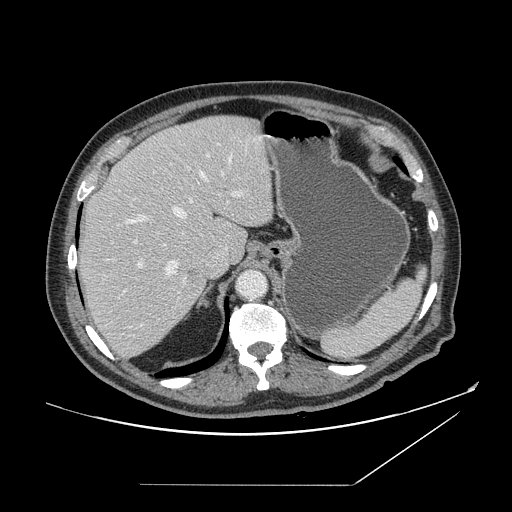
Contrast-enhanced abdominal CT, one axial slice; slice 115 of 166 in the series (ordered by position); intravenous contrast given; soft-tissue window (W 400 / L 40 HU); 2.5 mm slice thickness; 512 × 512 image matrix. Male patient, age 80 years. Case-level facts recorded for this patient, not image findings: diagnosis: colorectal cancer liver metastases, imaged before liver resection; multiple liver metastases: no; largest metastasis: 2.2 cm; disease in both lobes: no.
Annotated regions visible in this slice (manually delineated by an expert):
- hepatic veins: box from (x=124, y=156) to (x=232, y=277) px
- liver: (x=78, y=116)–(x=274, y=358)
- planned liver remnant (the part of the liver to remain after resection): (x=83, y=115)–(x=273, y=263)
- portal vein (with intrahepatic branches): (x=136, y=155)–(x=242, y=325)
- liver metastasis: (x=187, y=271)–(x=197, y=277)